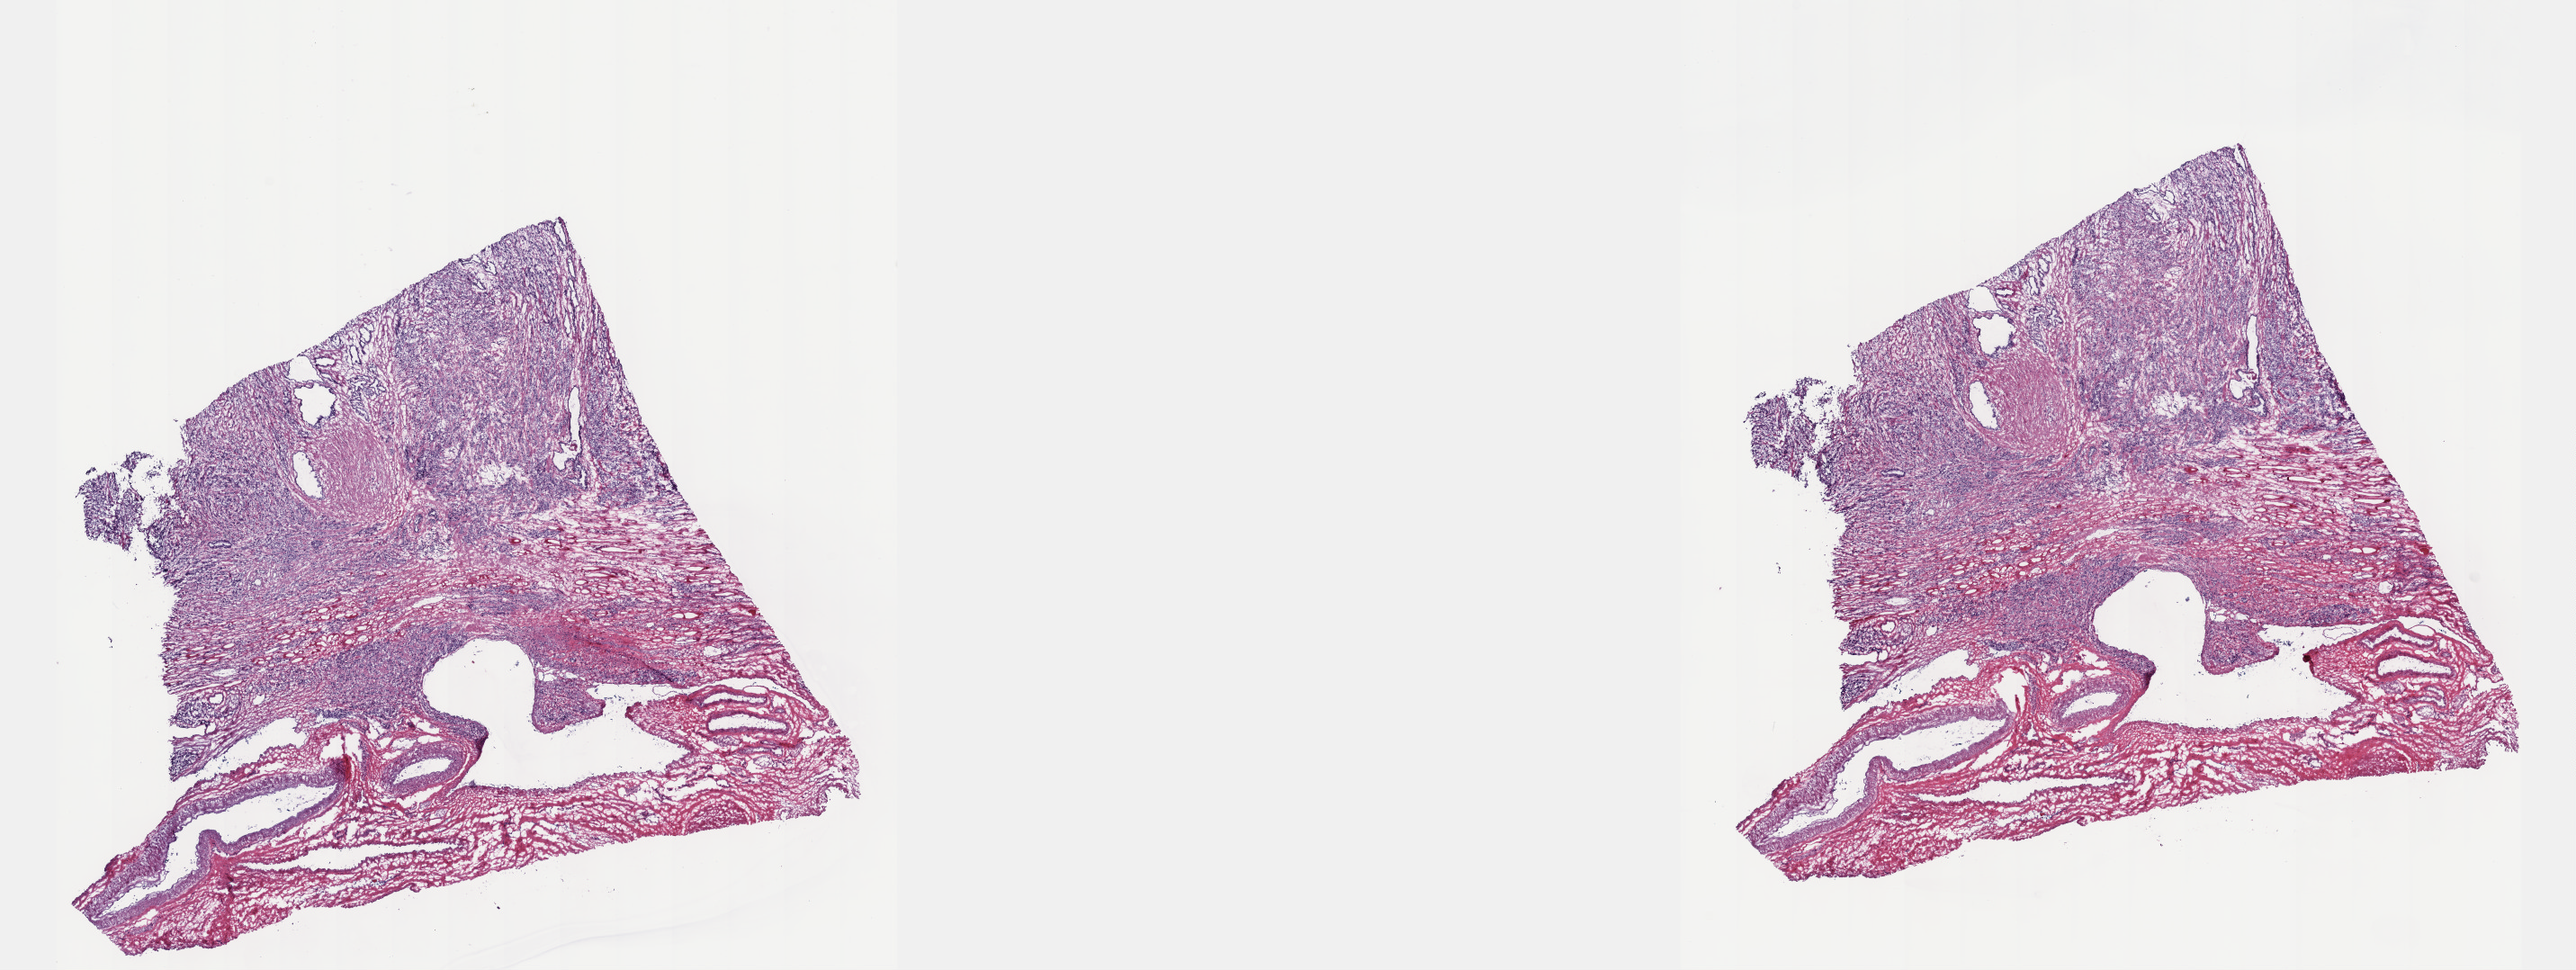
Digitized H&E-stained tissue section (whole slide) — low-resolution overview of the scanned area, about 23.1 x 8.7 mm (from a 40x scan); frozen section; prostate, primary tumour sample. Male, age 60 years at initial diagnosis. Gleason score: 9 (5+4). Slide review estimates, as recorded: tumour cells 50%, tumour nuclei 90%, normal cells 3%, stromal cells 46%, necrosis 1%. Infiltration values recorded for this section: lymphocyte infiltration 5%, monocyte infiltration 0%, neutrophil infiltration 0%.
Lymph nodes positive (case pathology): 0 of 15 examined. Diagnosis: Adenocarcinoma, NOS (prostate gland).